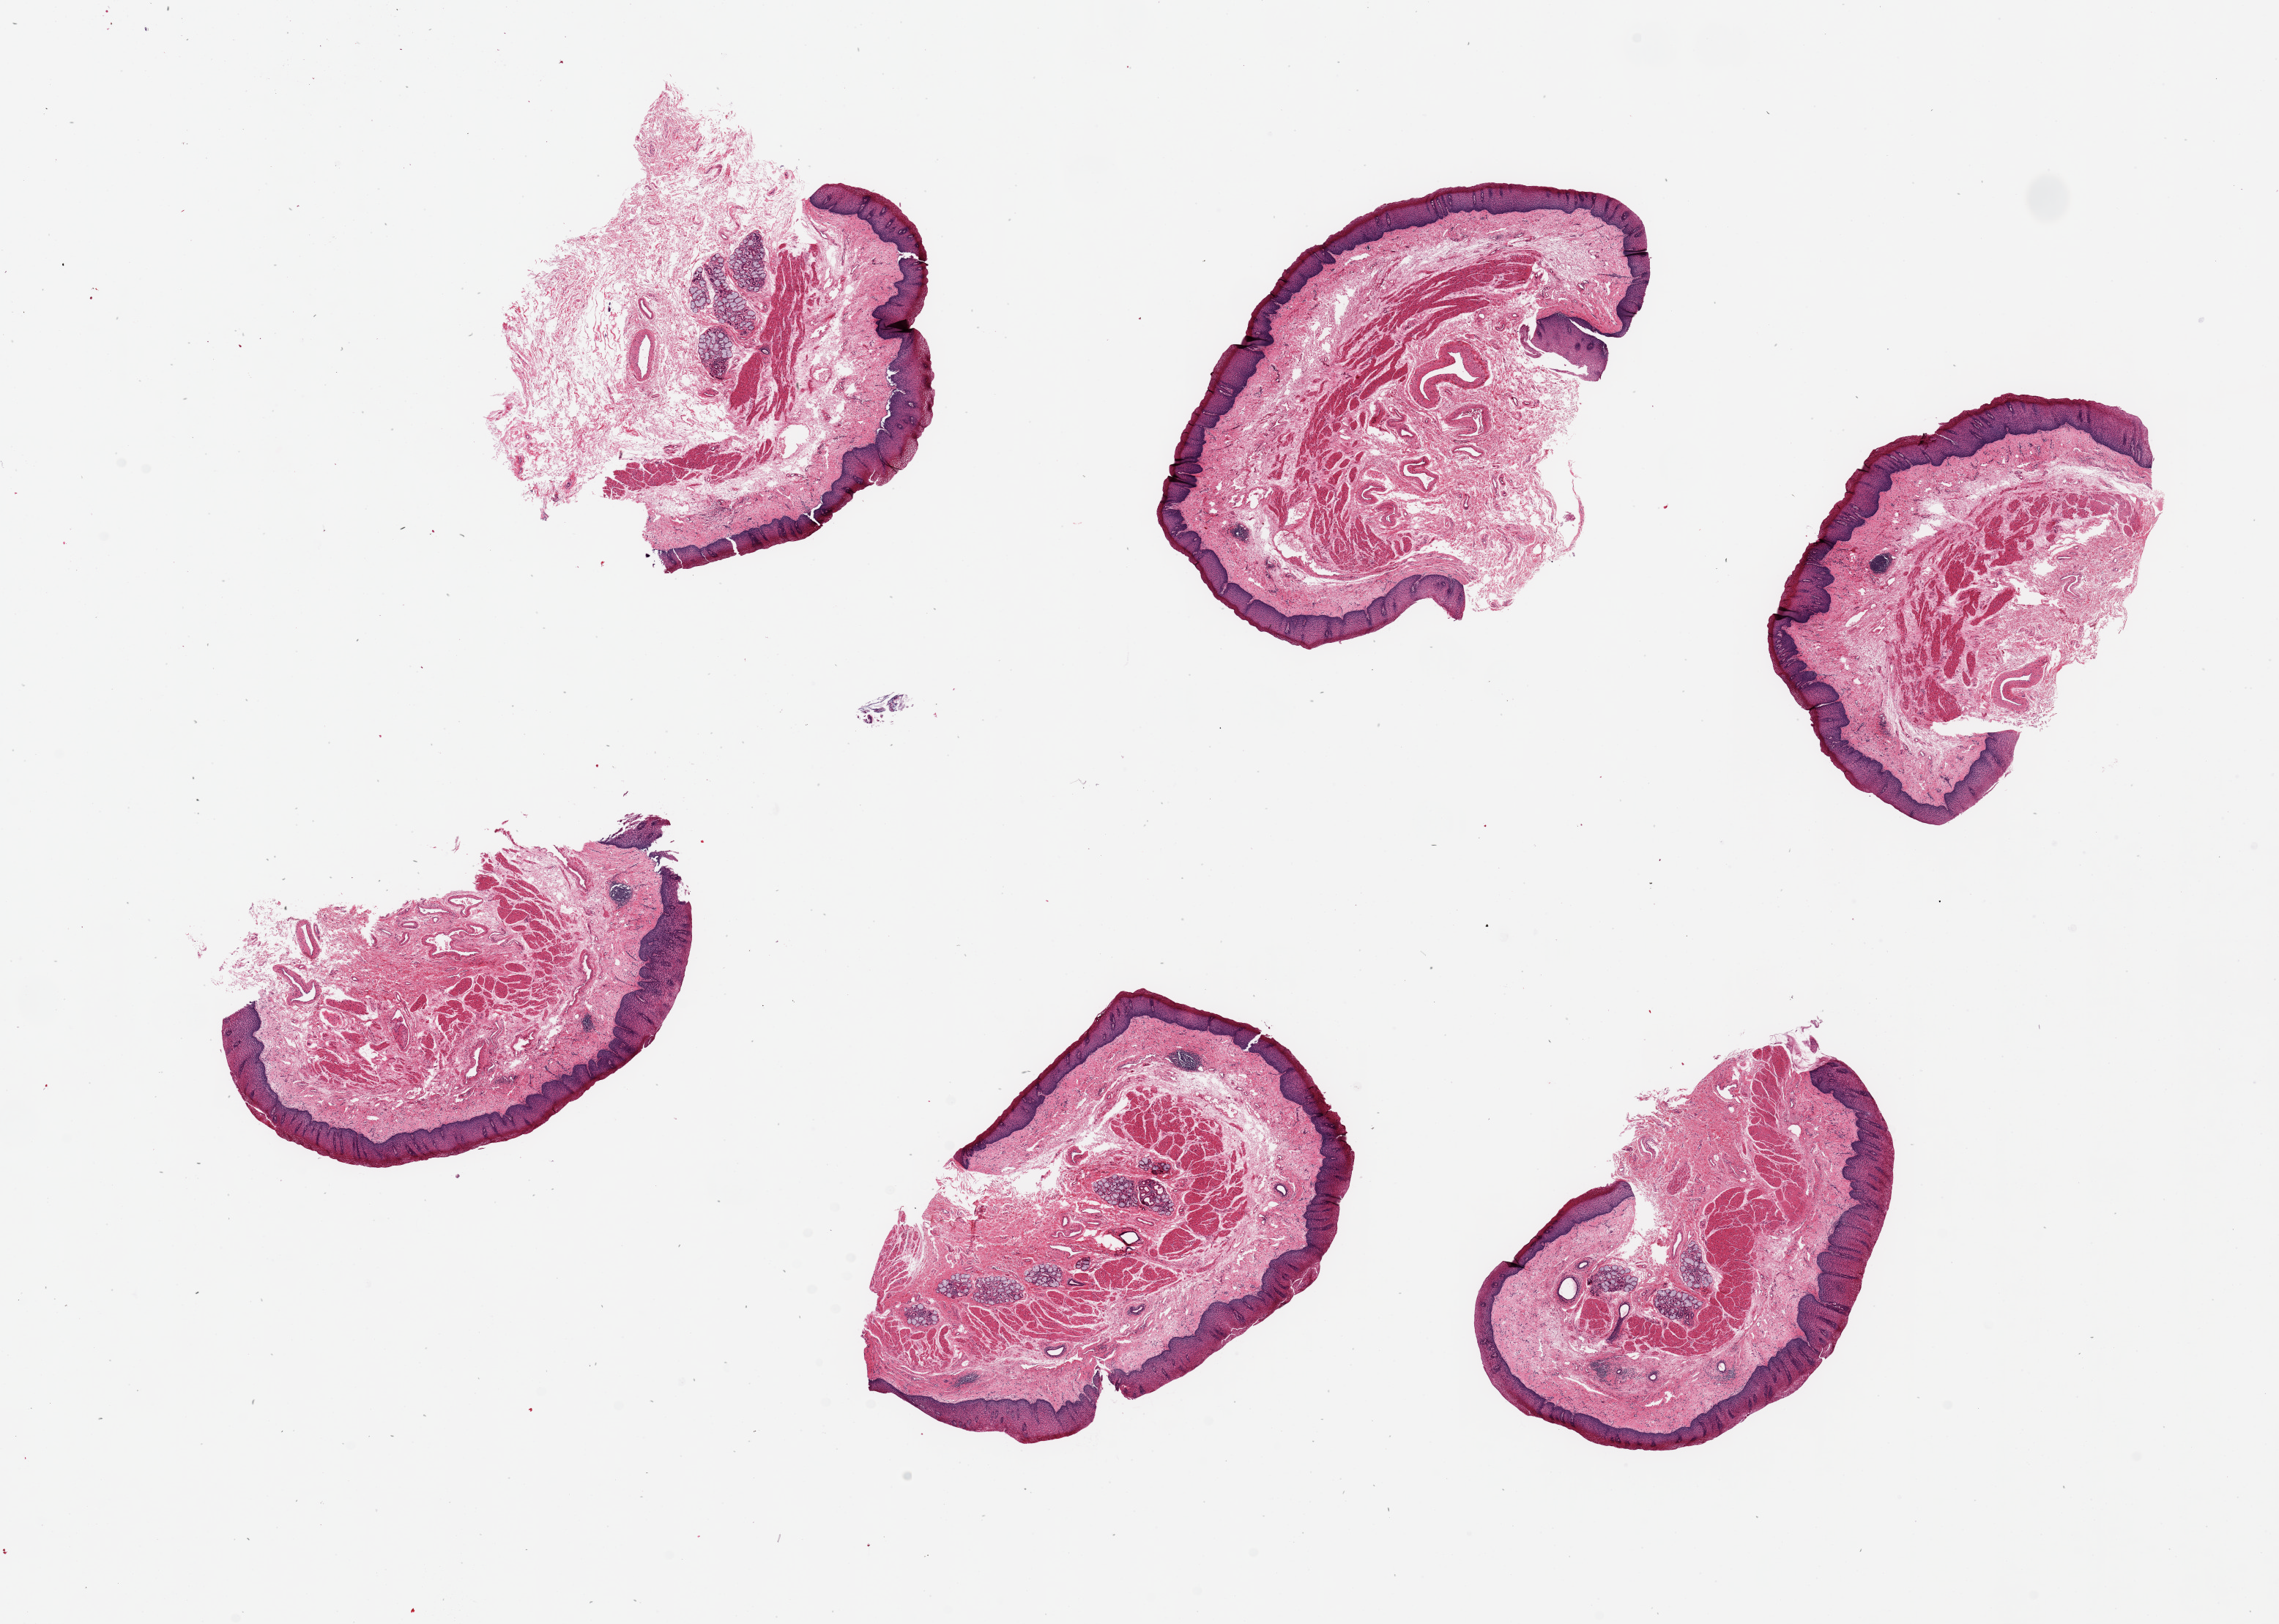
Digitized H&E-stained section, whole scanned area (about 24.6 x 17.5 mm) shown as a low-resolution overview; PAXgene-fixed paraffin-embedded (PFPE) section; target tissue: esophageal mucous membrane; donor tissue sample. Donor: male.
Review note (as recorded): 6 pieces ~6x4mm, squamous mucosa is ~10% thickness, representative intramural mucus glands.